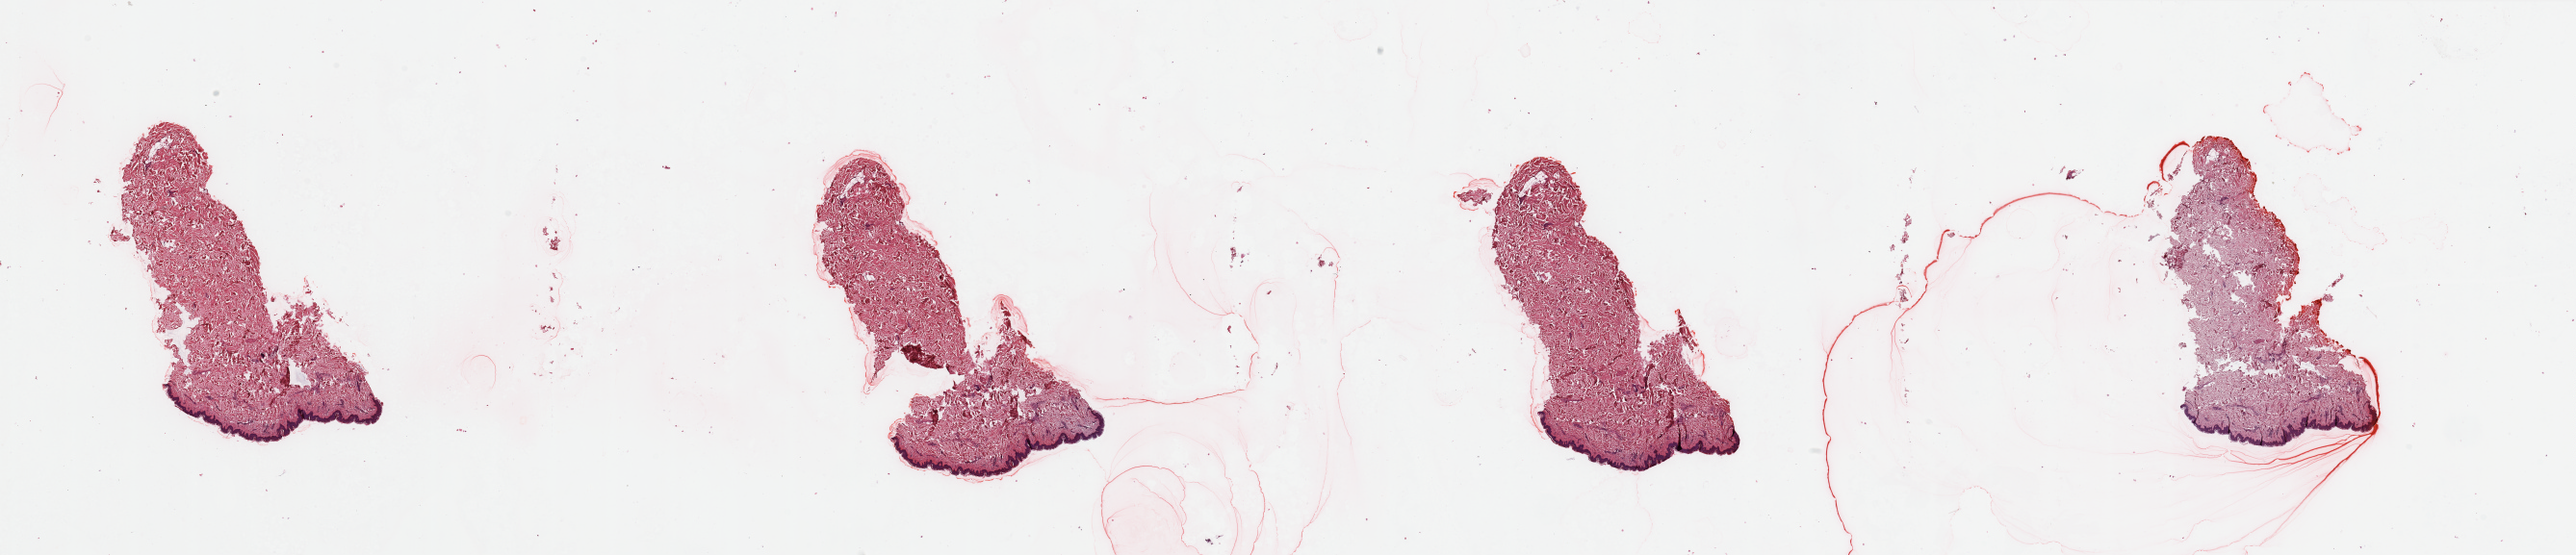
Whole-slide histology image, Hematoxylin and eosin (H&E) stained — whole scanned area (about 42.3 x 9.1 mm, from a 20x scan) shown as a low-resolution overview; normal (non-tumour) tissue sample, sampled site: trunk. Male, 42 y/o.
• this section: normal (non-tumour) tissue from the same patient
• patient diagnosis: Malignant melanoma, NOS